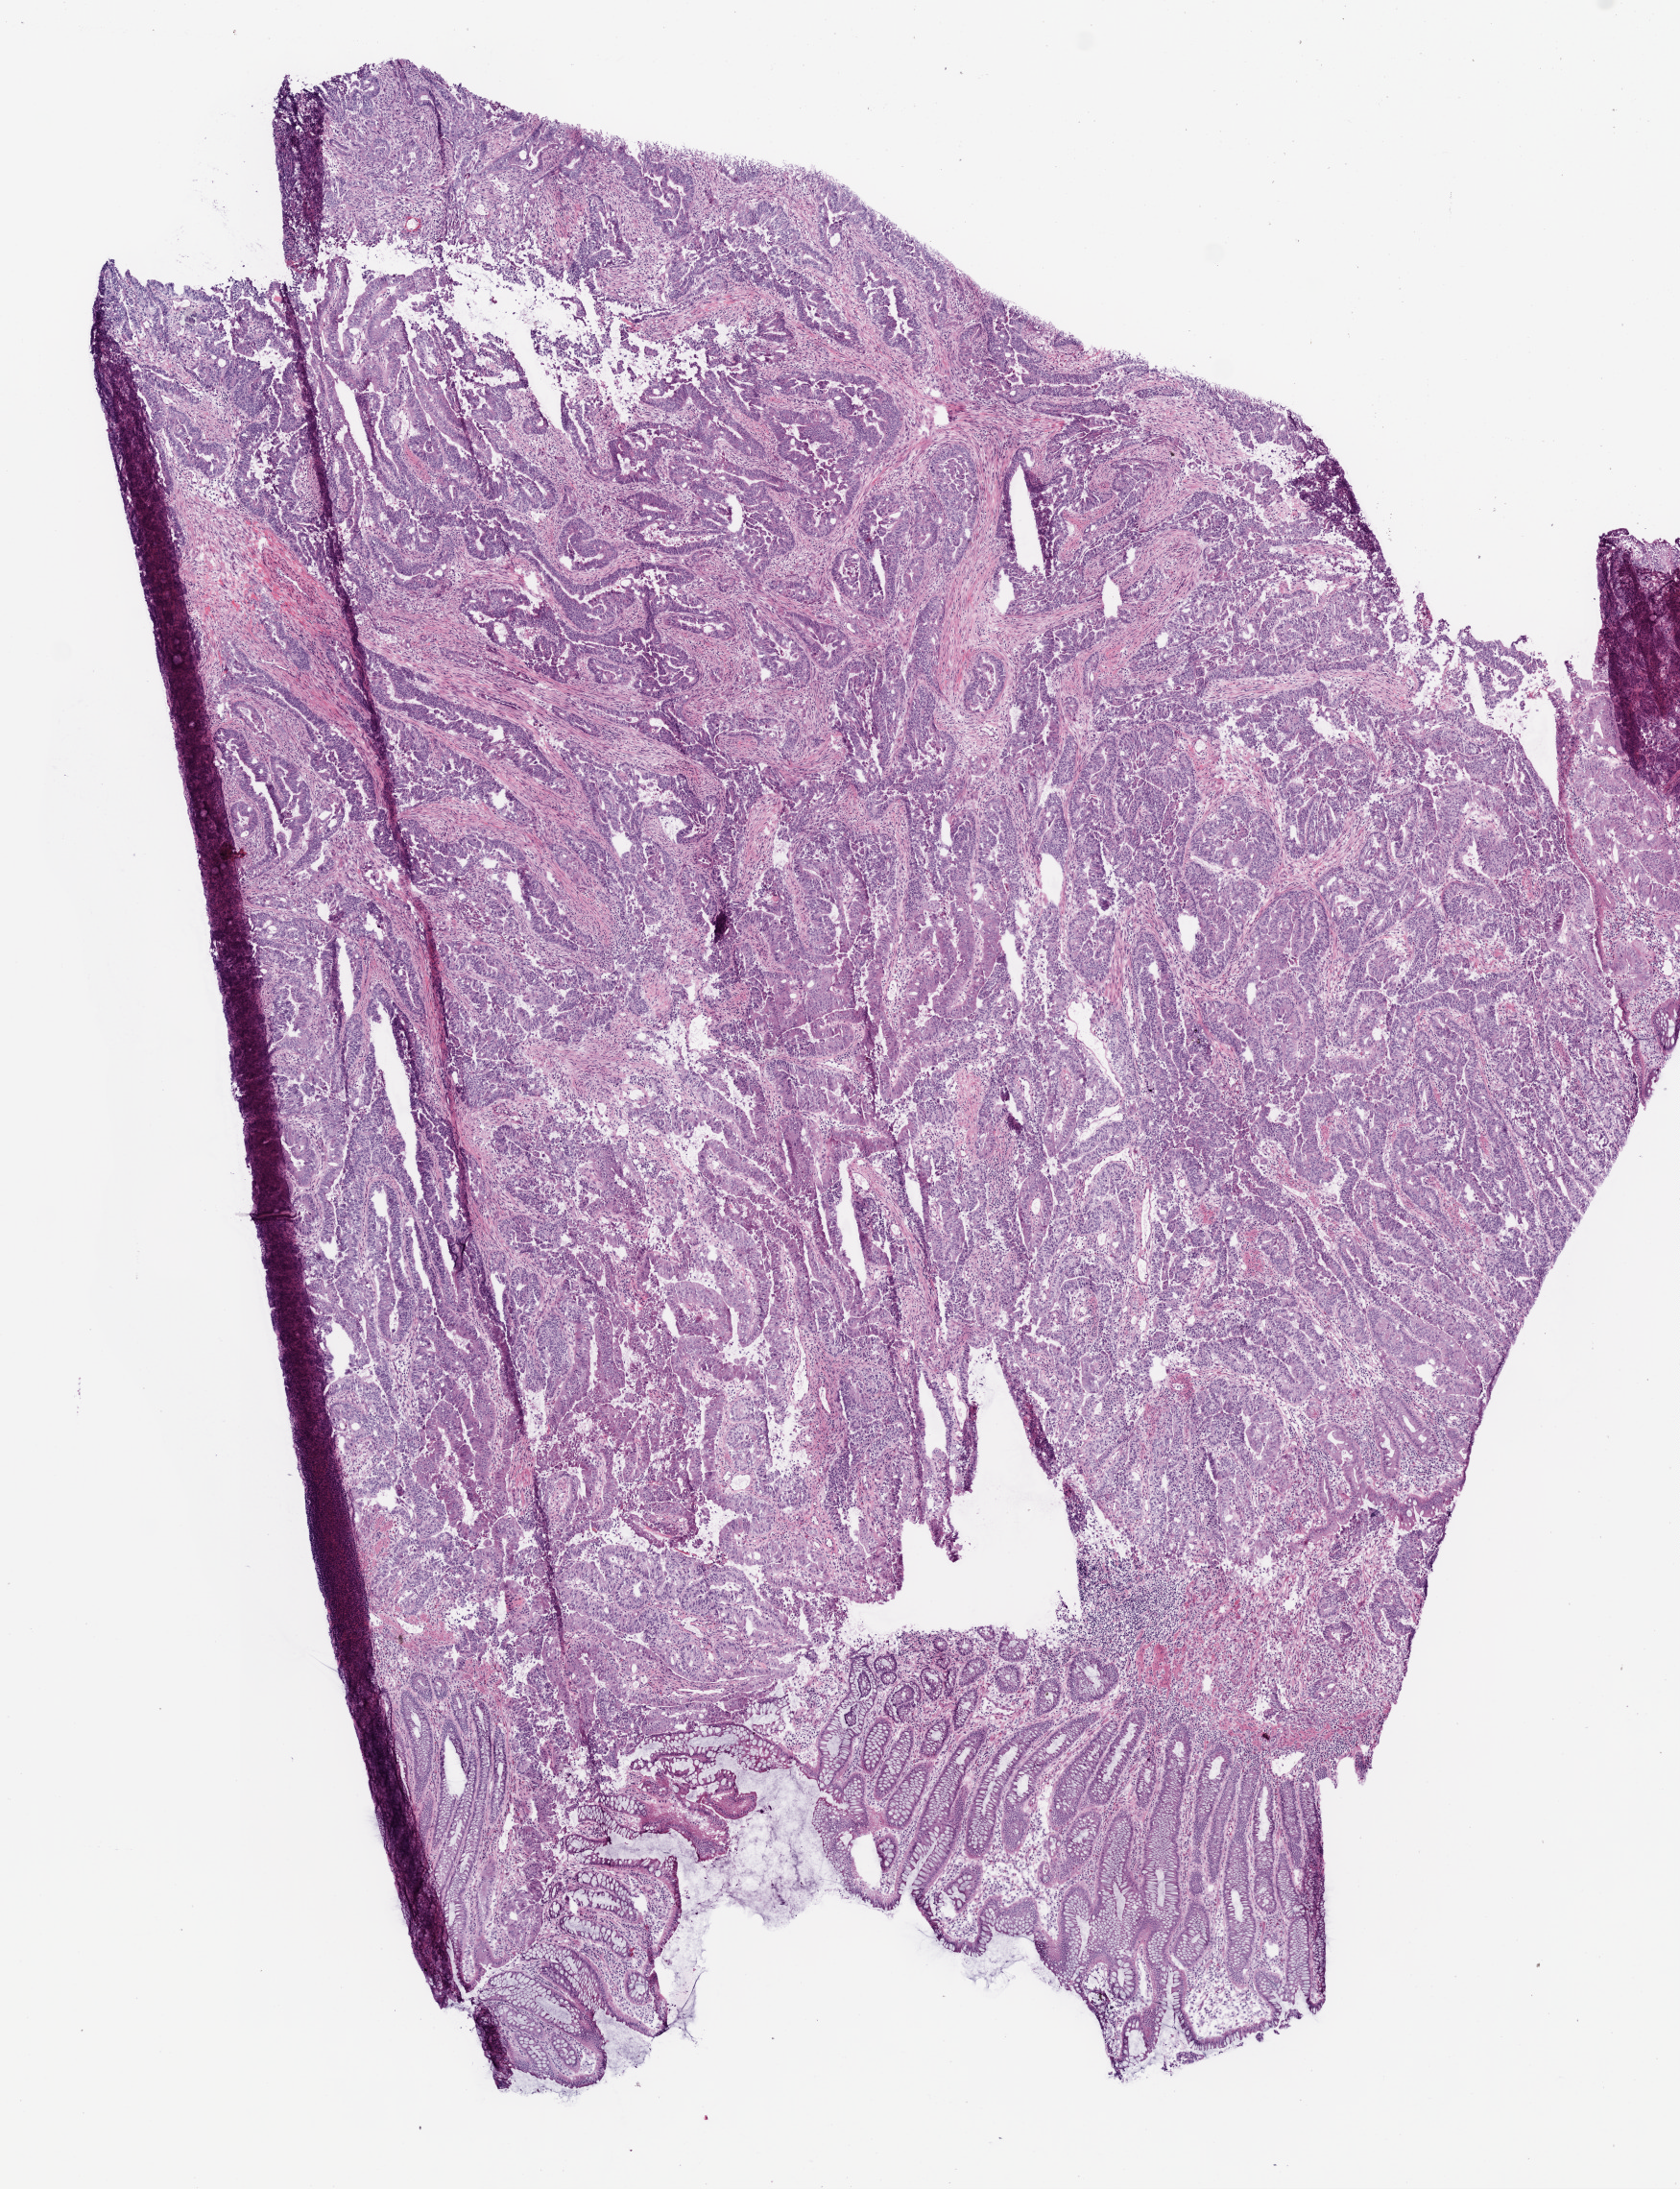
Digitized Hematoxylin and eosin (H&E) stained tissue section (whole slide) — whole scanned area (about 7.0 x 9.1 mm, from a 20x scan) shown as a low-resolution overview. Frozen section from the bottom of the tissue portion. Sample: primary tumour, rectum. Patient: female, age at initial diagnosis 66 years. Composition of this section per pathologist review: tumour cells 80%, tumour nuclei 80%, normal cells 15%, stromal cells 5%, necrosis 0%.
• histologic diagnosis: Adenocarcinoma, NOS (rectosigmoid junction)
• AJCC pathologic stage: IIIC (6th edition)
• TNM: T3 N2 M0